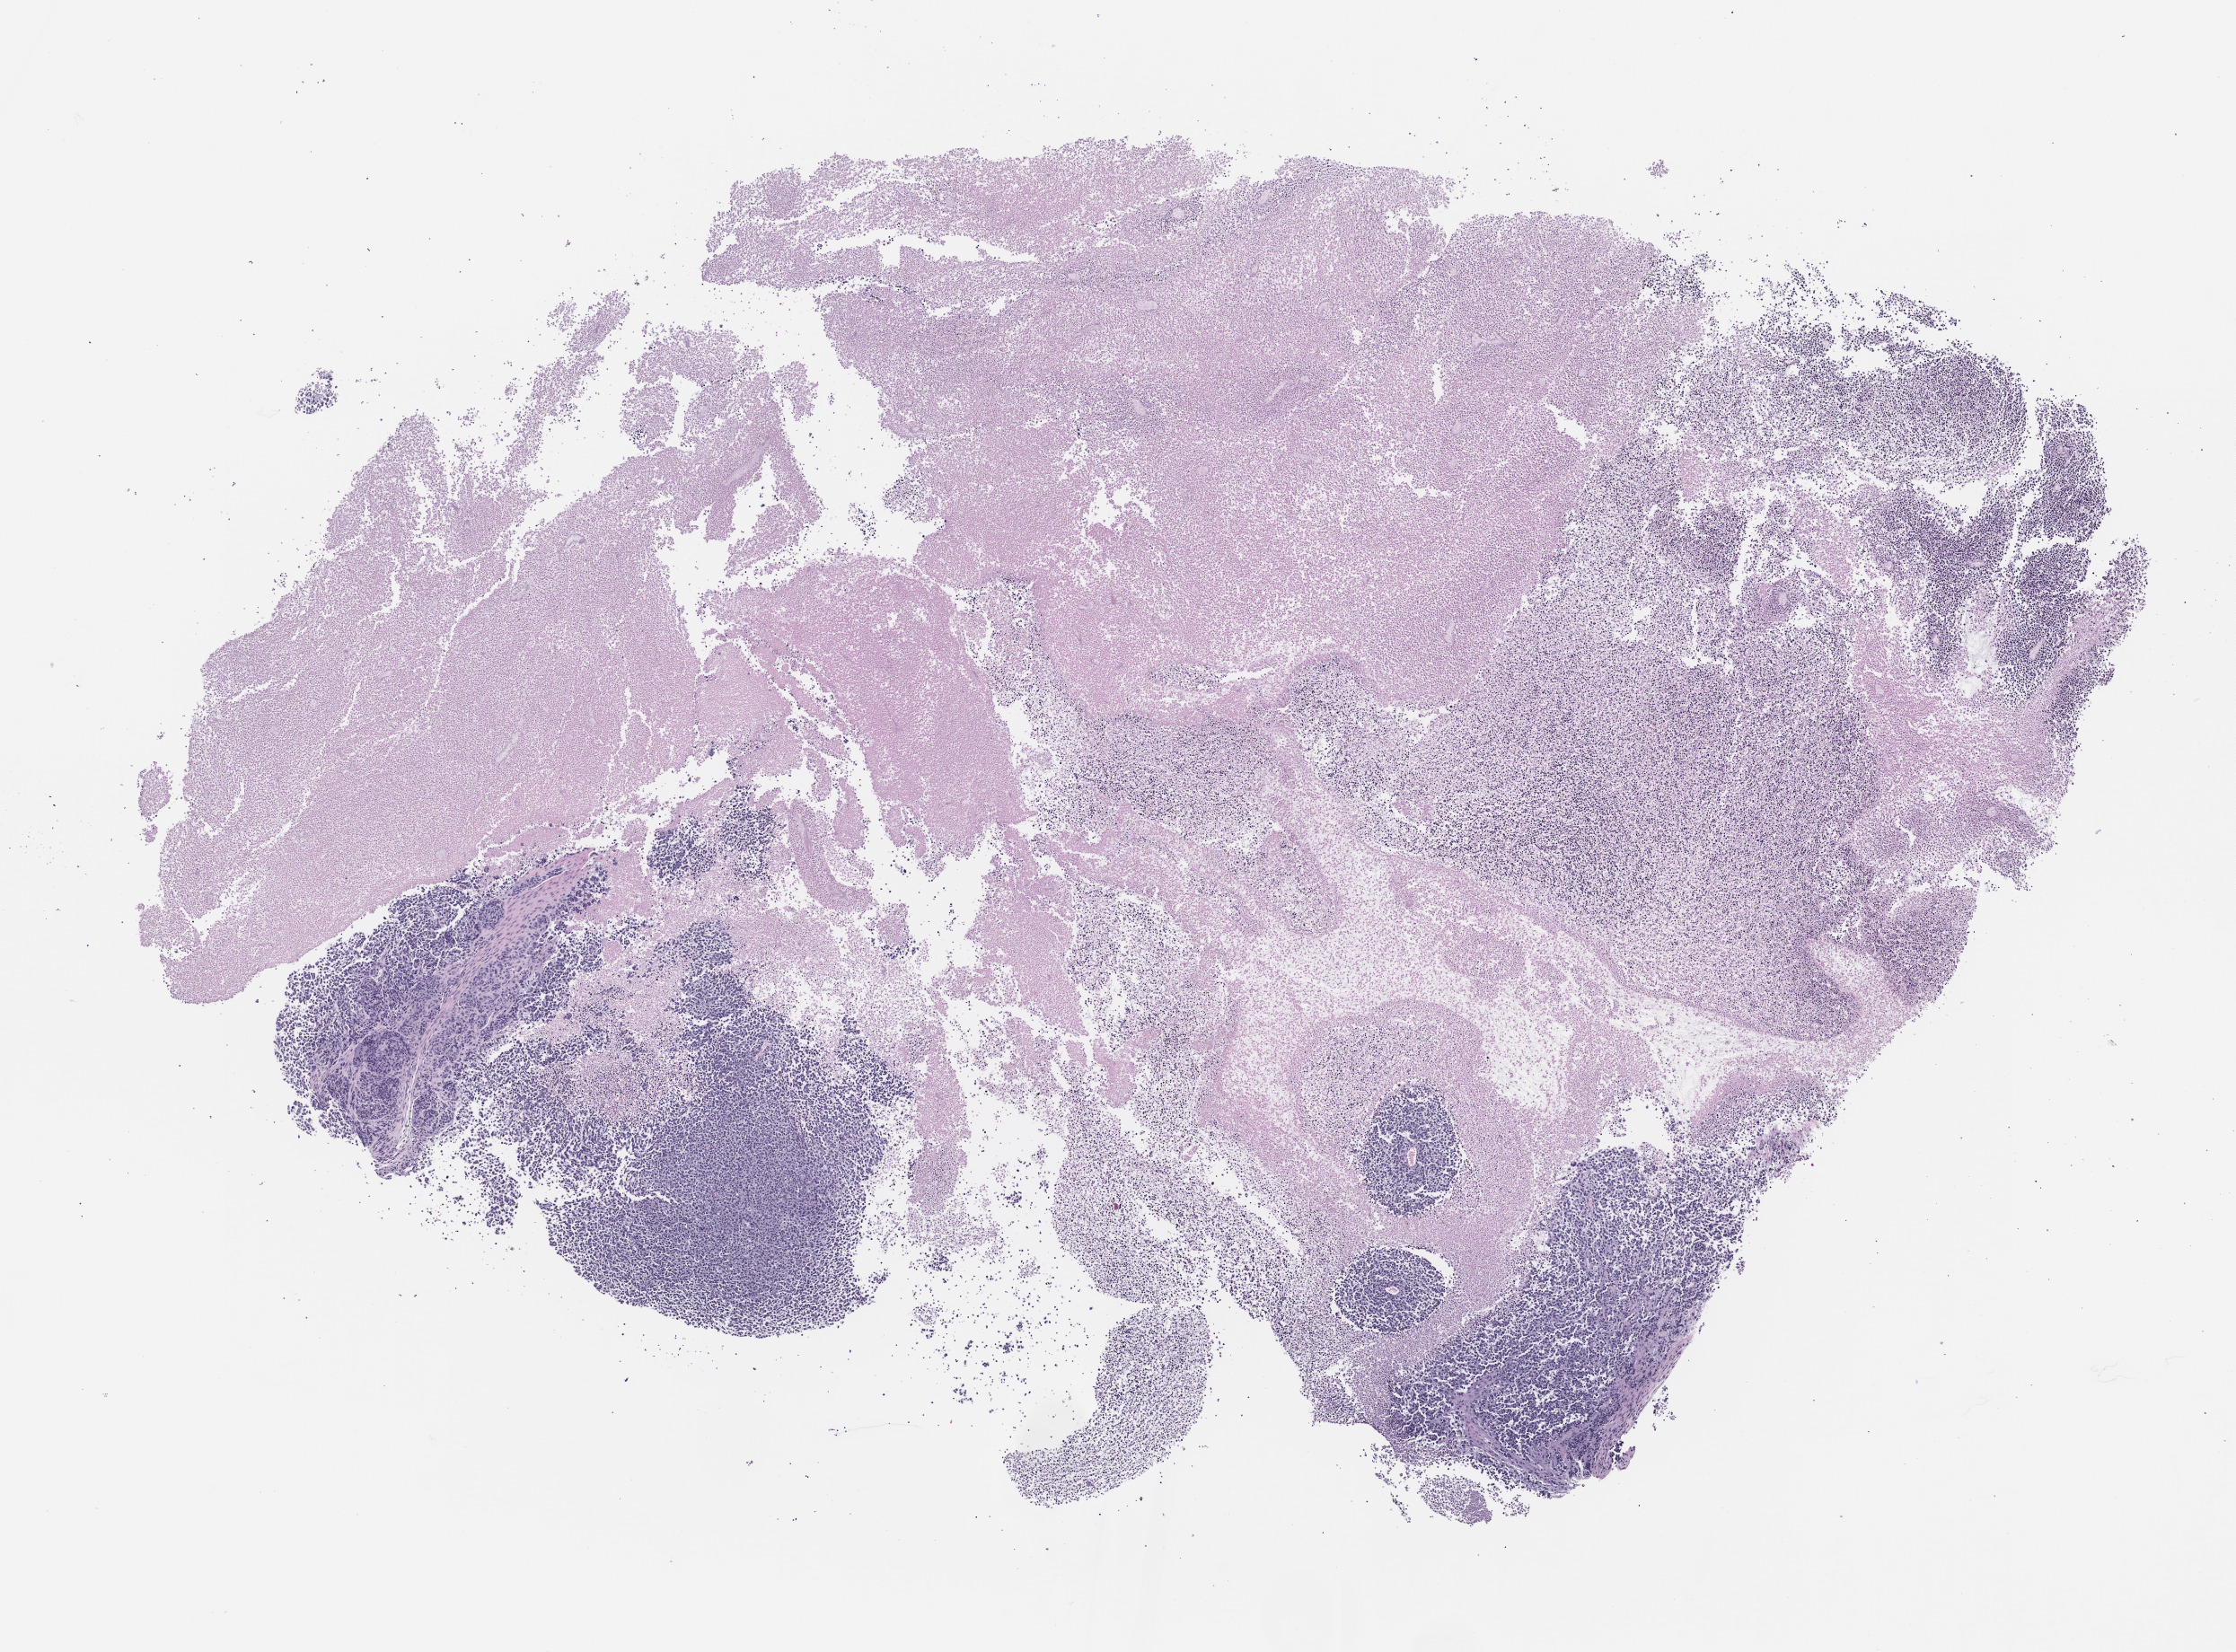
Haematoxylin and eosin whole-slide image of a patient-derived xenograft (PDX) tumor grown in a mouse, passage 2 — whole scanned area (about 10.0 x 7.4 mm) shown as a low-resolution overview. Formalin-fixed paraffin-embedded section. Tumor site category: musculoskeletal.
Originating patient diagnosis: Ewing Sarcoma|Primitive Neuroectodermal Tumor.